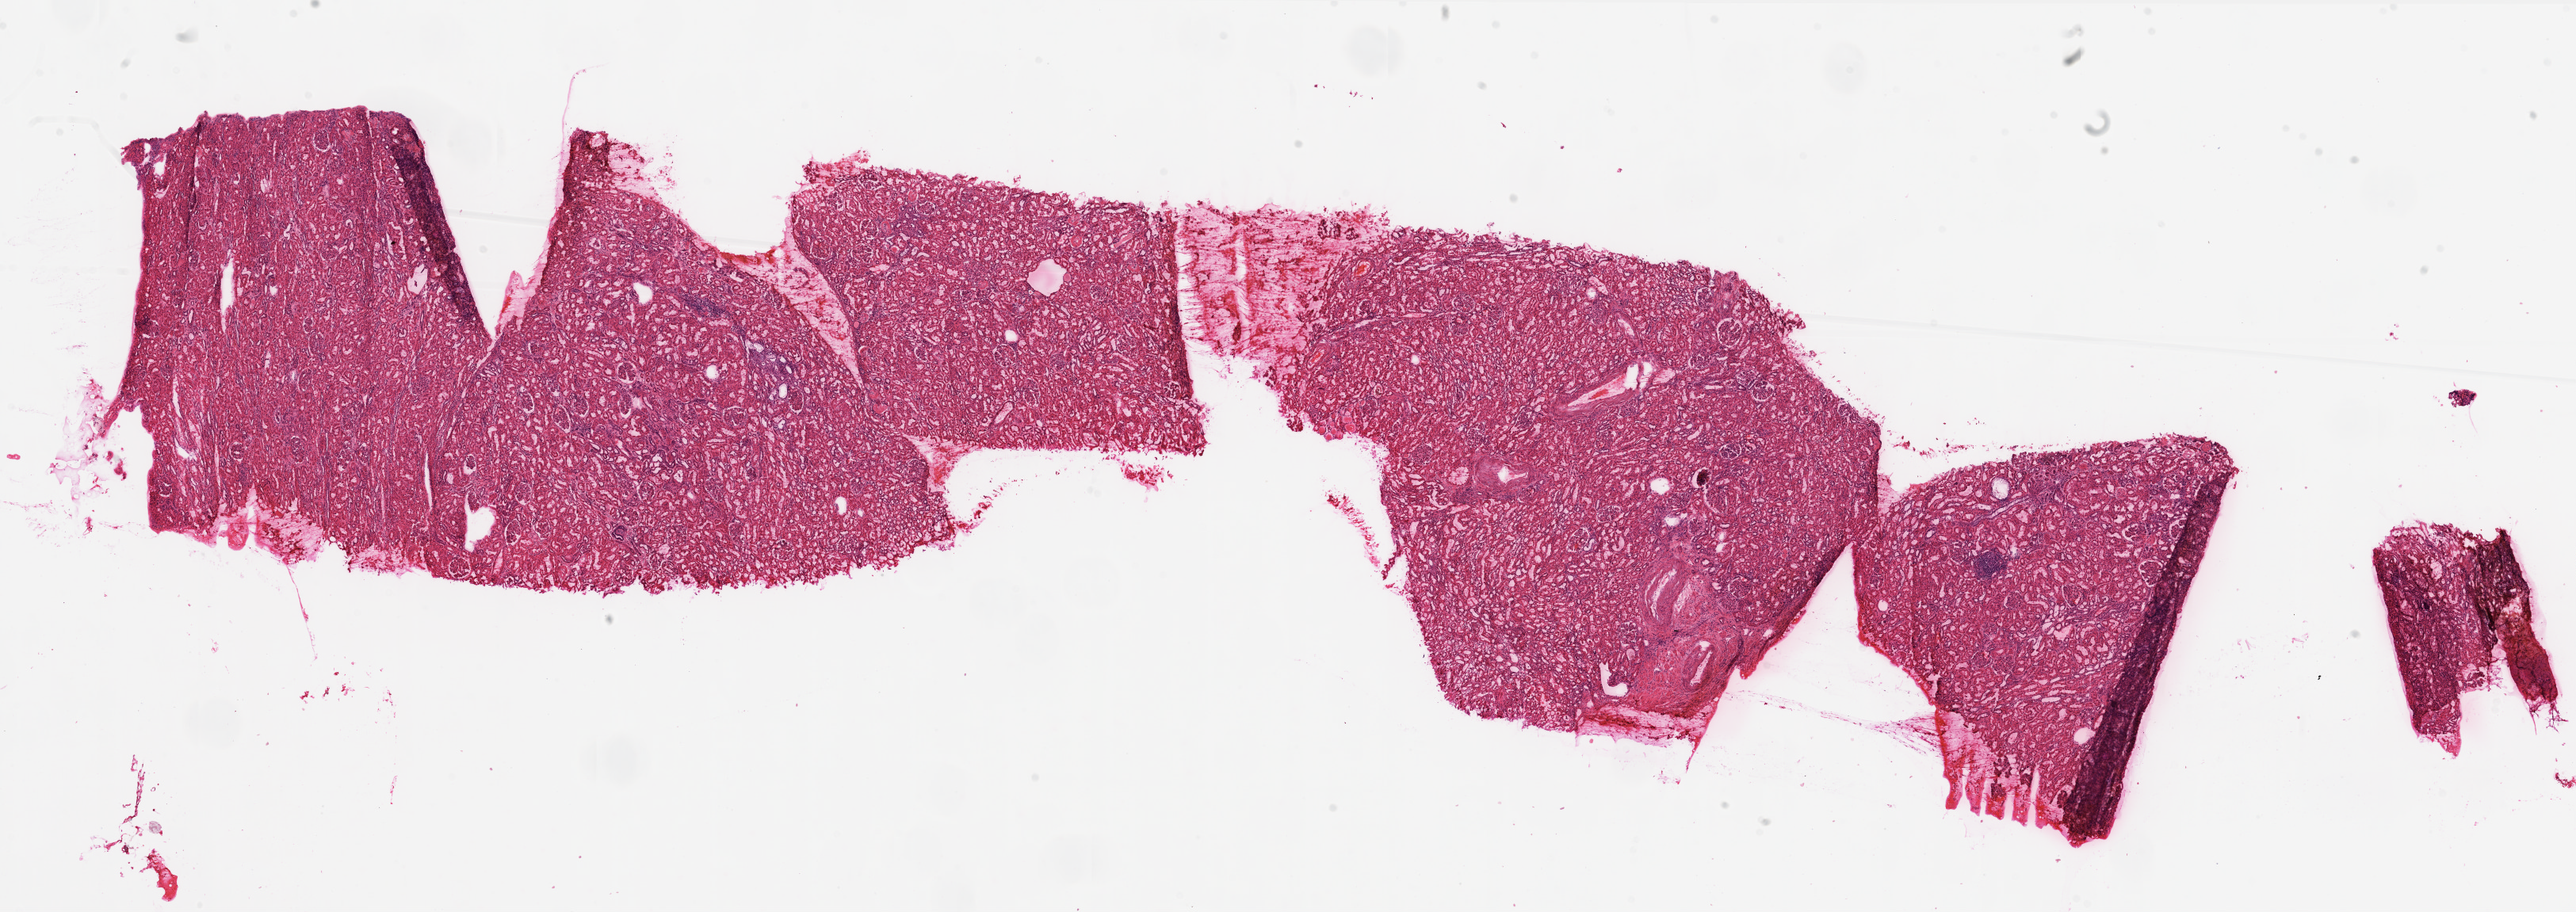
H&E-stained whole-slide image, shown as a low-resolution overview of the whole scanned area (about 26.1 x 9.2 mm, slide scanned at 20x). Frozen section from the top of the tissue portion. Kidney, solid tissue normal (non-tumour tissue) sample. Female patient; age at initial diagnosis 73 years.
This section: solid tissue normal (non-tumour) sample from the same patient. Patient diagnosis: Clear cell adenocarcinoma, NOS.